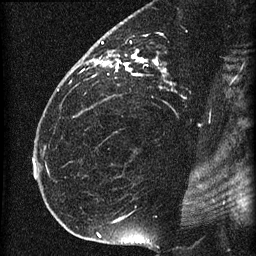
Breast MRI (dynamic contrast-enhanced), one sagittal slice; position 41 of 60 along the scan axis; dynamic contrast-enhanced series, image 2 of 4 at this slice position (ordered by acquisition); 1.5 T; TE 4.2 ms, TR 22.7 ms; 1.5 mm slice thickness; 256 × 256 image matrix. Female patient, age 35 years. From the clinical record (not read from this slice): setting: breast cancer imaged before/during neoadjuvant chemotherapy; receptor status: HR-positive, HER2-negative.
Structures marked on this image (semi-automatically segmented with operator editing):
- analysis volume of interest (the breast-tissue region the enhancement analysis was run in; not a lesion): bounding box <69,27,199,112> (left, top, right, bottom; pixels)
- tumour enhancement mask (voxels above the 90 % enhancement threshold inside the analysis volume of interest): <88,41,173,84>